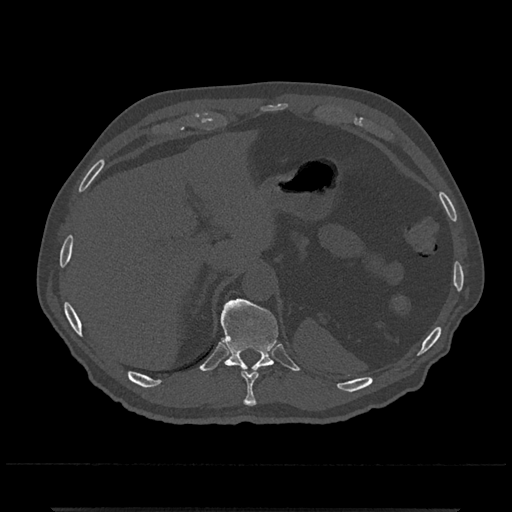
CT including the spine, one axial slice. Slice 516 of 797 in the series (ordered by position). Reconstruction kernel Br40s/3. Bone window (W 1800 / L 400 HU). 0.5 mm slice thickness. 512 × 512 image matrix, field of view 393 × 393 mm. Male patient, age 67 years. From the clinical record (not read from this slice): primary cancer: prostate.
Annotated regions visible in this slice (semi-automatically segmented with operator editing):
- T10 vertebra: bounding box [x1, y1, x2, y2] px = [241, 369, 259, 407]
- T11 vertebra: [221, 299, 278, 372]